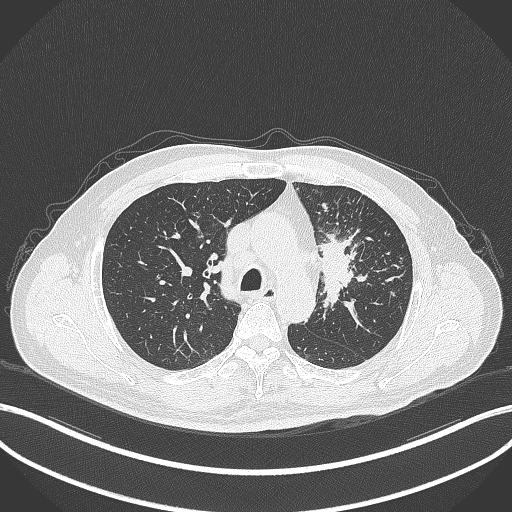
Chest CT, one axial slice; slice 244 of 386 in the series (ordered by position); 120 kVp; lung window (W 1500 / L -600 HU); 1 mm slice thickness; 512 × 512 image matrix. Patient: male, 69 years. From the clinical record (not read from this slice): clinical TNM (as recorded): T2a N2 M0; histopathological grade: G2-3.
Outlined on this slice (bounding box drawn by a radiologist):
- lung tumour (recorded histology: adenocarcinoma): bounding box <313,228,361,316> (left, top, right, bottom; pixels)